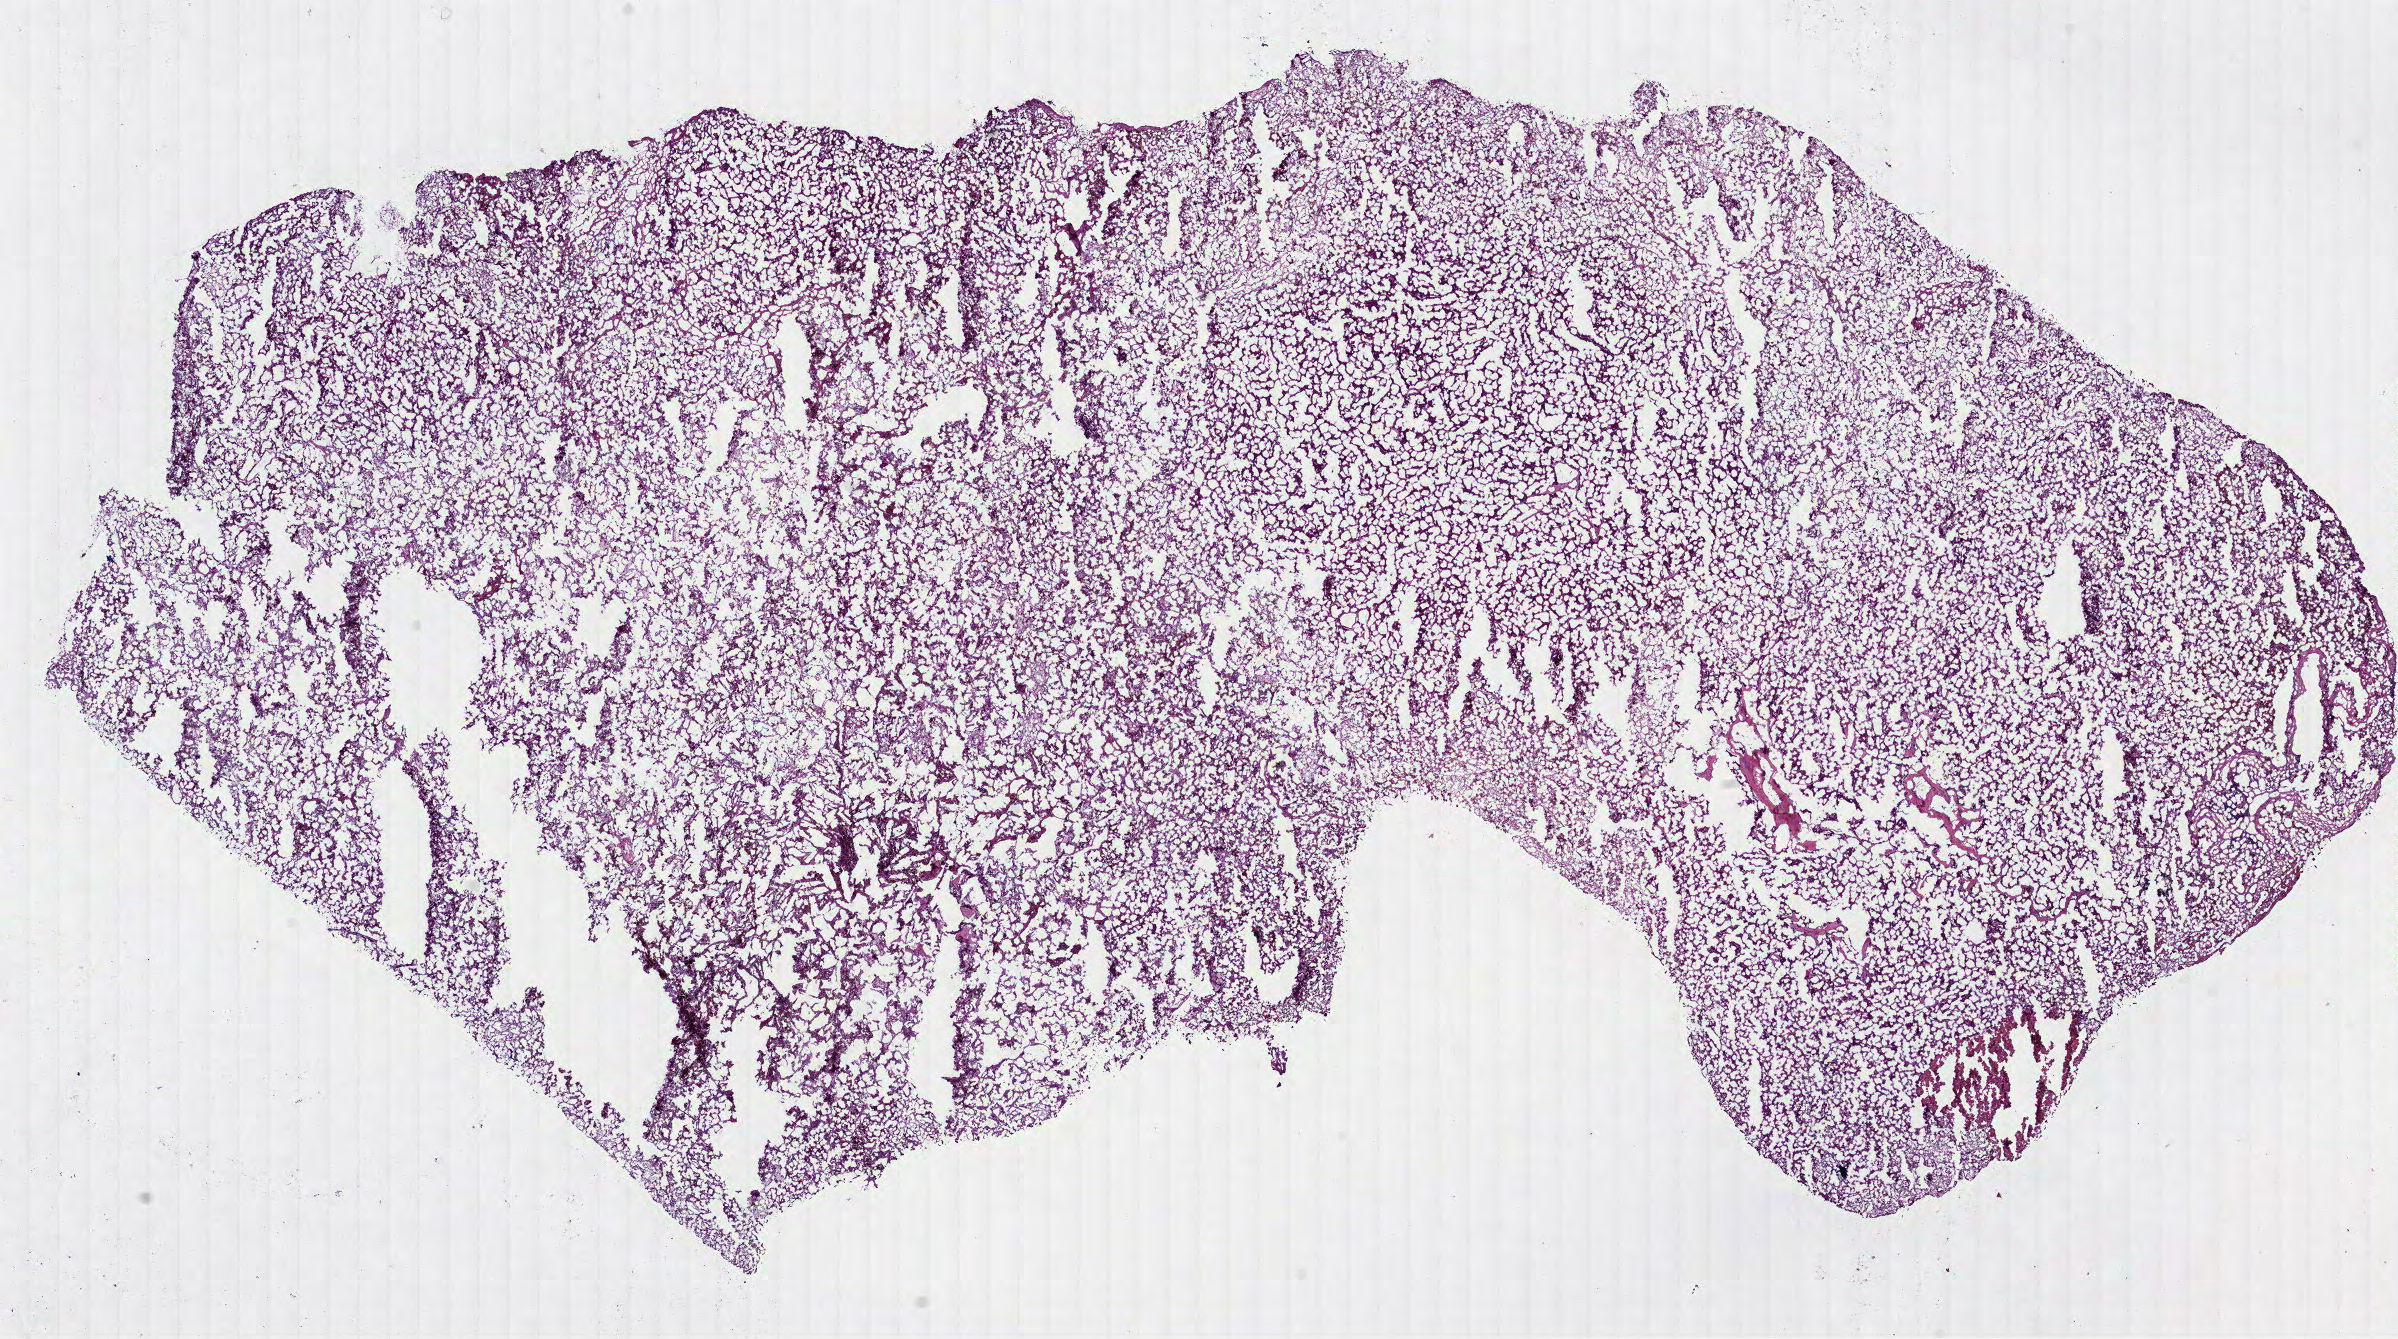
H&E-stained whole-slide image — a low-resolution overview of the entire scanned area, about 19.3 x 10.8 mm (from a 40x scan), frozen section from the bottom of the tissue portion, sample: primary tumour, kidney. Male patient; age at initial diagnosis 69 years. Slide review estimates, as recorded: tumour cells 95%, tumour nuclei 80%, normal cells 0%, stromal cells 5%, necrosis 0%.
TNM: T1a NX M0. AJCC pathologic stage: I. Pathologic diagnosis: Papillary adenocarcinoma, NOS. Laterality: right.